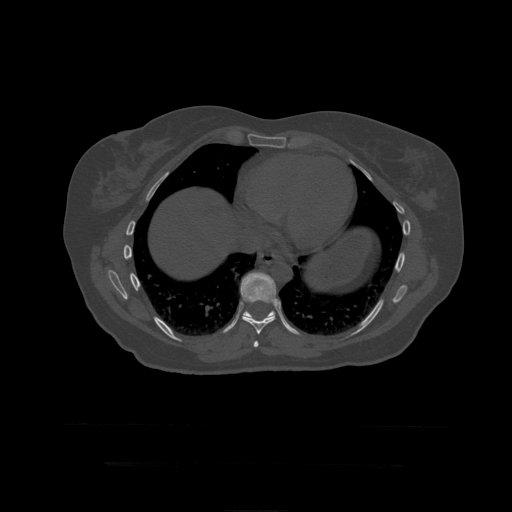
CT including the spine, one axial slice; slice 256 of 399 in the series (ordered by position); reconstruction kernel STANDARD; 120 kVp; bone window (W 1800 / L 400 HU); 1.25 mm slice thickness; 512 × 512 image matrix. Patient age 41 years. From the clinical record (not read from this slice): primary cancer: breast.
Outlined on this slice (semi-automatic segmentation, software-assisted and operator-edited):
- T10 vertebra: bounding box [x1, y1, x2, y2] px = [242, 300, 276, 320]
- T8 vertebra: [254, 341, 259, 348]
- T9 vertebra: [241, 272, 280, 335]